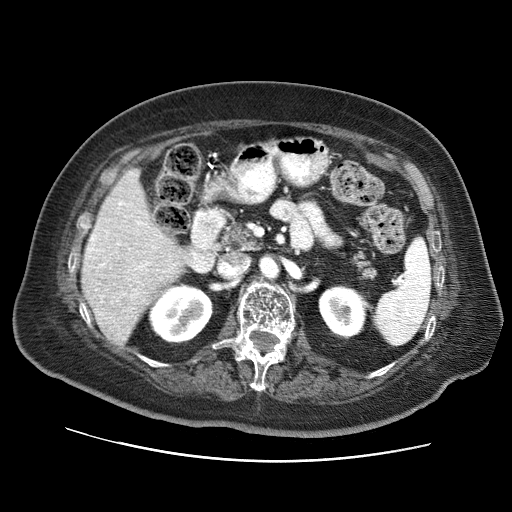
Contrast-enhanced abdominal CT (liver protocol), one axial slice; position 30 of 73 along the scan axis; reconstruction kernel STANDARD; 120 kVp; soft-tissue window (W 400 / L 40 HU); 2.5 mm slice thickness; 512 × 512 image matrix. Case-level facts recorded for this patient, not image findings: diagnosis: hepatocellular carcinoma (patient treated with transarterial chemoembolisation; whether this scan precedes or follows treatment is not stated here); TNM stage (as recorded): Stage-I; Child-Pugh class: A; tumour differentiation: well differentiated; tumour nodularity: uninodular.
Outlined on this slice (semi-automatic segmentation, software-assisted and operator-edited):
- liver parenchyma outside the tumour (the mass and vessels are separate outlines, so this box may not span the whole liver): bounding box (x1, y1, x2, y2) in pixels: (82, 168, 180, 345)
- liver vessels: (88, 201, 172, 302)